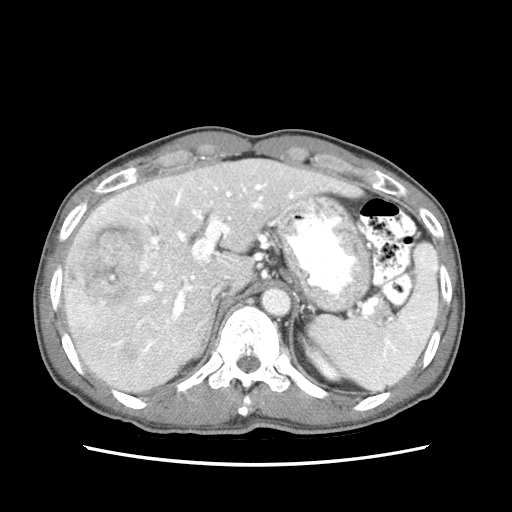
Contrast-enhanced abdominal CT (liver protocol), one axial slice. Reconstruction kernel STANDARD. 120 kVp. Soft-tissue window (W 400 / L 40 HU). 2.5 mm slice thickness. 512 × 512 image matrix, field of view 320 × 320 mm. Case-level facts recorded for this patient, not image findings: diagnosis: hepatocellular carcinoma (patient treated with transarterial chemoembolisation; whether this scan precedes or follows treatment is not stated here); TNM stage (as recorded): Stage-IIIB; Child-Pugh class: A; tumour differentiation: moderately differentiated.
Outlined on this slice (semi-automatic segmentation, software-assisted and operator-edited):
- liver parenchyma outside the tumour (the mass and vessels are separate outlines, so this box may not span the whole liver): box from (x=64, y=158) to (x=360, y=392) px
- mass: (x=64, y=209)–(x=141, y=332)
- liver vessels: (x=98, y=169)–(x=342, y=368)